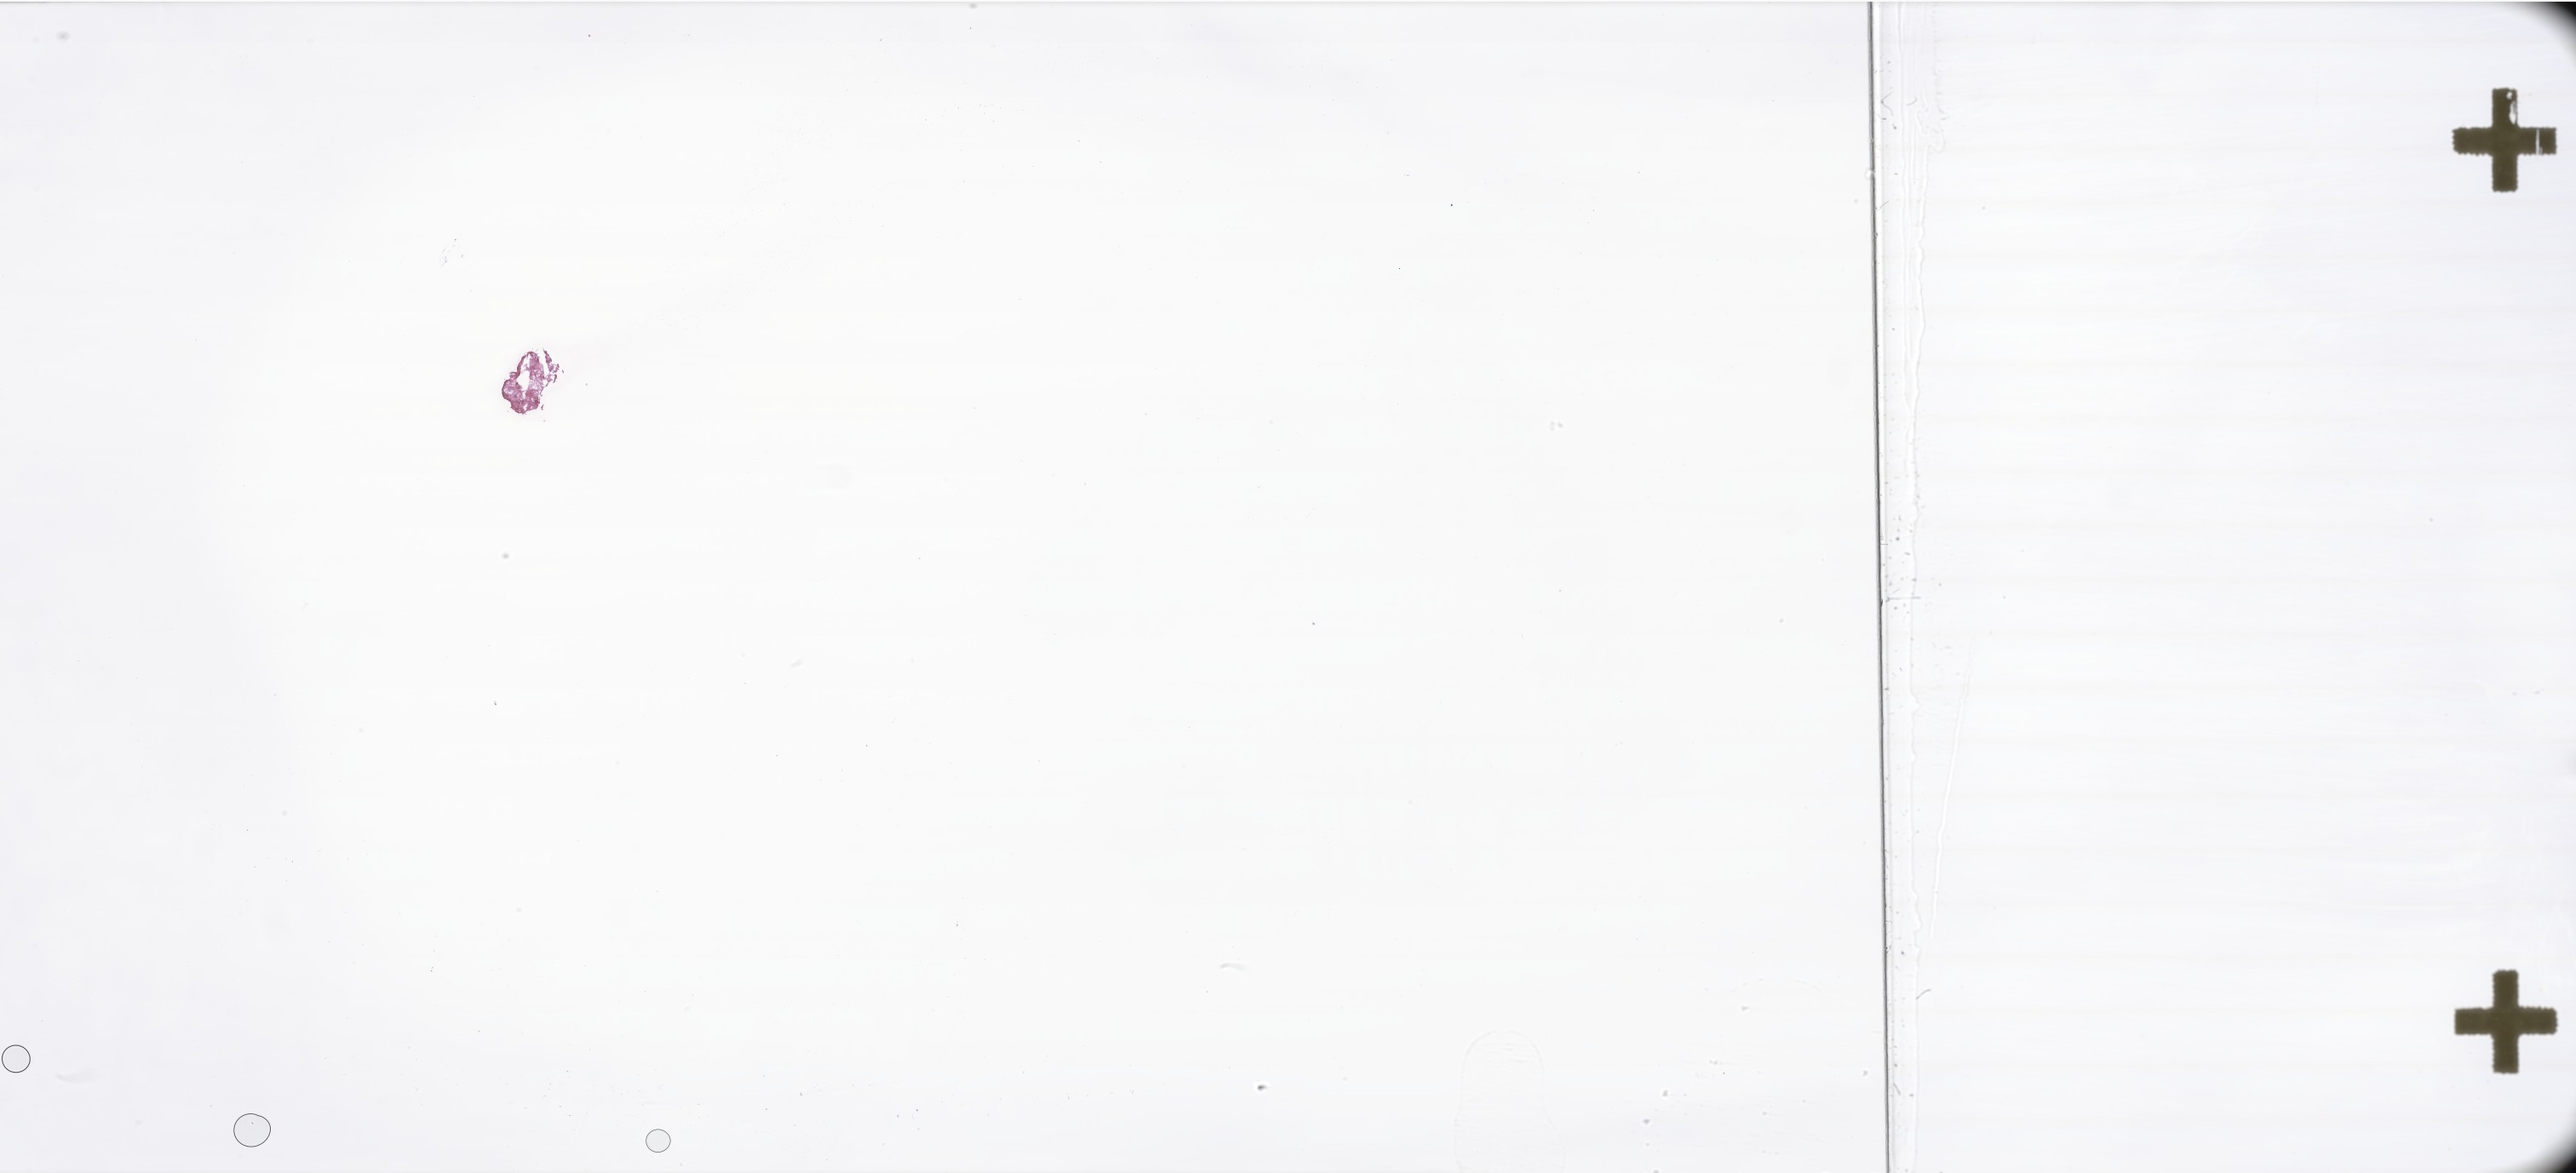
Whole-slide image, H&E stain of tumor tissue from the brain — low-resolution overview of the scanned area, about 51.0 x 23.2 mm, frozen section (OCT-embedded). Patient male; age 117 months.
Recorded diagnosis: Pilocytic astrocytoma.